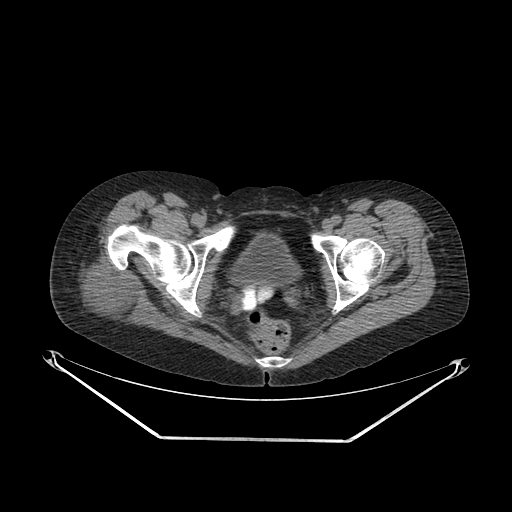
CT of an extremity soft-tissue mass (from a PET/CT study), one axial slice. Slice 48 of 267 in the series (ordered by position). 140 kVp. Soft-tissue window (W 400 / L 40 HU). 3.75 mm slice thickness. 512 × 512 image matrix. Female patient. Case-level facts recorded for this patient, not image findings: histological type: epithelioid sarcoma with vascular differentiation; site of the primary tumour: right buttock.
Structures marked on this image (expert contour drawn on MRI and transferred to this co-registered scan by the dataset authors):
- gross tumour volume (mass): bounding box <69,258,154,330> (left, top, right, bottom; pixels)